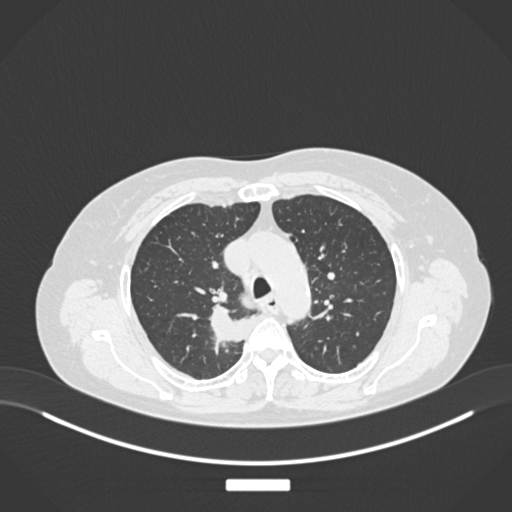
Chest CT, one axial slice. Slice 188 of 237 in the series (ordered by position). Reconstruction kernel B30f. Lung window (W 1500 / L -600 HU). 1 mm slice thickness. 512 × 512 image matrix, field of view 400 × 400 mm. Female patient, age 62 years. From the clinical record (not read from this slice): clinical TNM (as recorded): T1c N1 M0.
Annotated regions visible in this slice (bounding box drawn by a radiologist):
- lung tumour (recorded histology: squamous cell carcinoma): box from (x=204, y=299) to (x=247, y=355) px